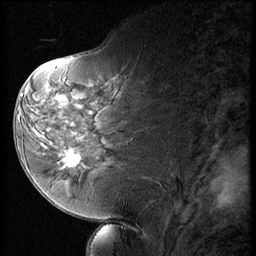
Breast MRI (dynamic contrast-enhanced), one sagittal slice. Position 28 of 56 along the scan axis. 3 images stored at this slice position (order not interpretable as contrast timing). 1.5 T. TE 4.2 ms, TR 9 ms. 2.5 mm slice thickness. 256 × 256 image matrix, field of view 180 × 180 mm. Female patient, age 58 years. Case-level facts recorded for this patient, not image findings: setting: breast cancer imaged before/during neoadjuvant chemotherapy; receptor status: HR-positive, HER2-negative.
Structures marked on this image (semi-automatic segmentation, software-assisted and operator-edited):
- analysis volume of interest (the breast-tissue region the enhancement analysis was run in; not a lesion): box from (x=47, y=136) to (x=88, y=178) px
- tumour enhancement mask (voxels above the 140 % enhancement threshold inside the analysis volume of interest): (x=61, y=153)–(x=80, y=168)